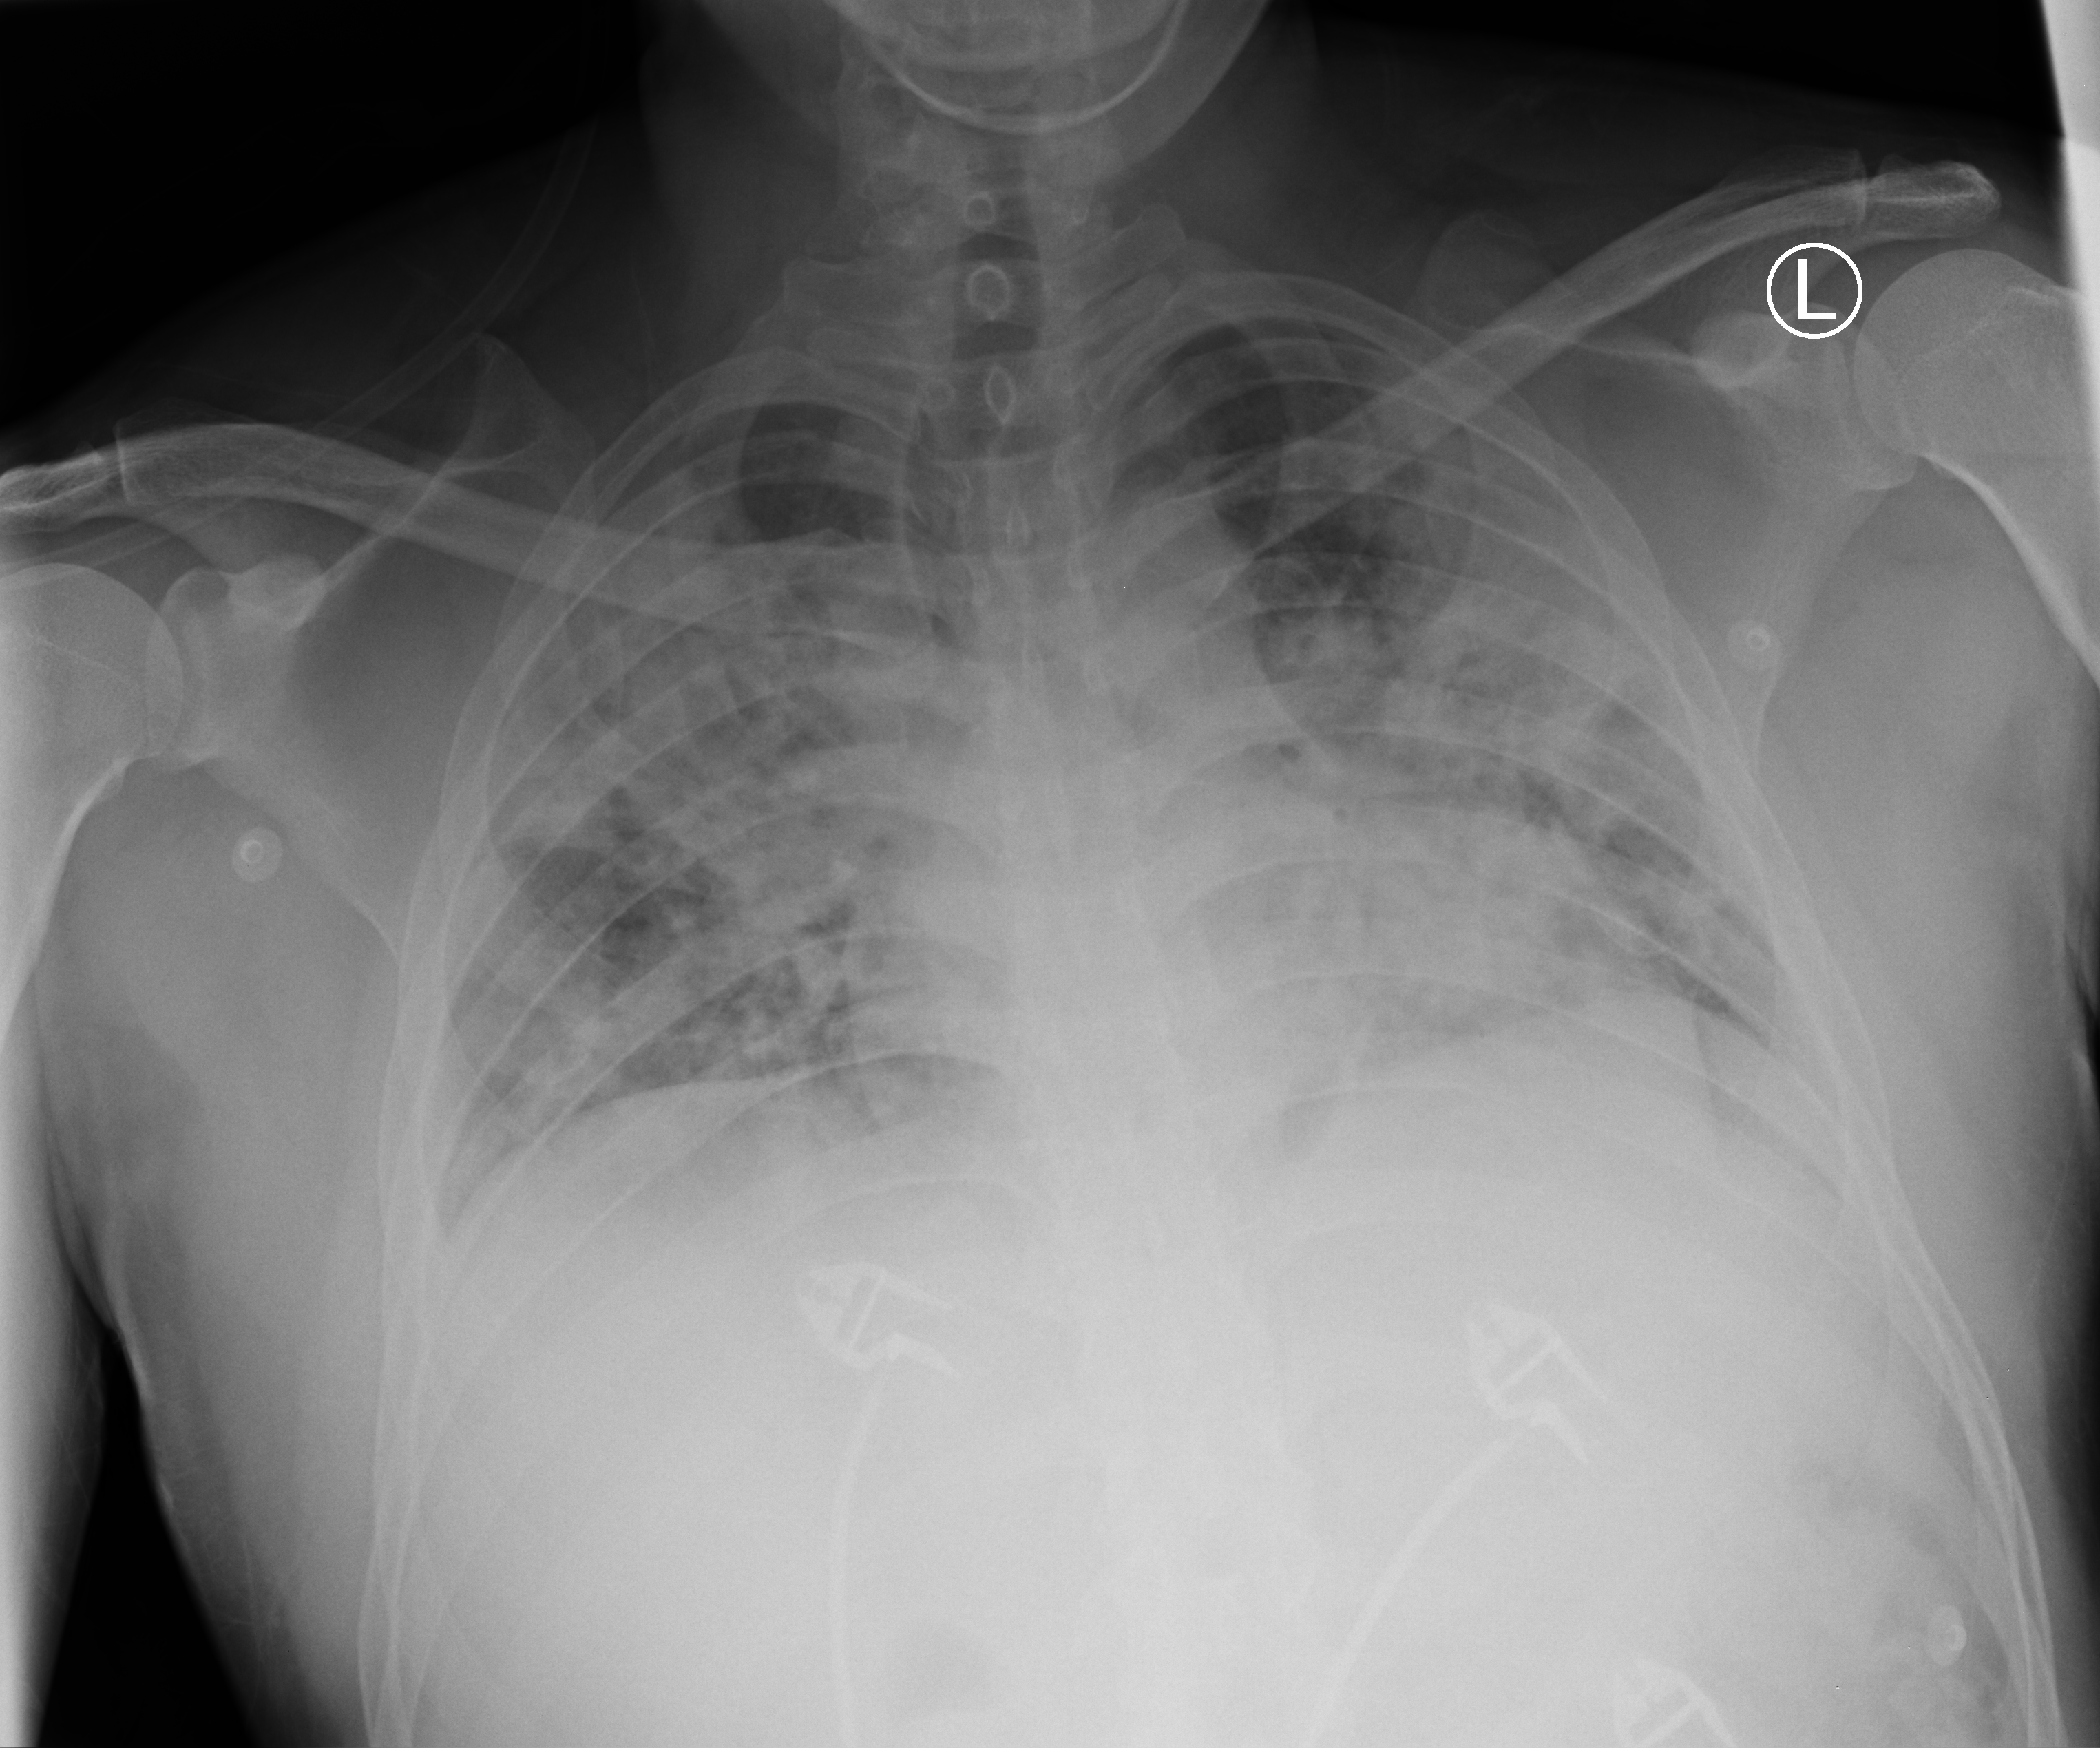
Chest X-ray (portable). Male patient hospitalised with COVID-19, age 18–59 years.
From the hospital-stay record, not from the radiograph (when in the stay this image was taken is not recorded): smoking status (admission record): never.